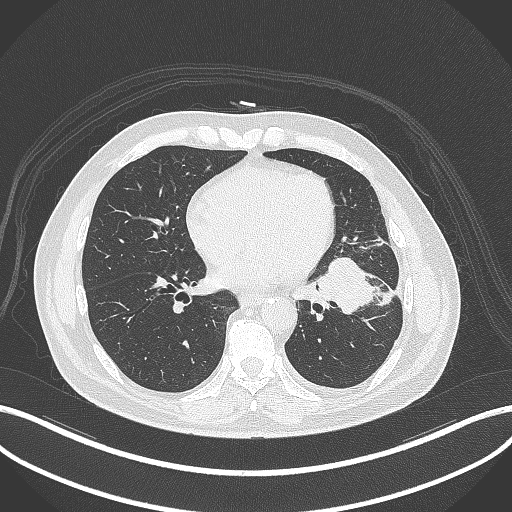
Chest CT, one axial slice. Position 148 of 230 along the scan axis. Reconstruction kernel B70f. 120 kVp. Lung window (W 1500 / L -600 HU). 1 mm slice thickness. 512 × 512 image matrix, field of view 400 × 400 mm. Patient: male, 68 years. Case-level facts recorded for this patient, not image findings: clinical TNM (as recorded): T2b N0 M0.
Structures marked on this image (rectangle marked by the reading radiologist):
- lung tumour (recorded histology: squamous cell carcinoma): bounding box [x1, y1, x2, y2] px = [314, 250, 380, 318]